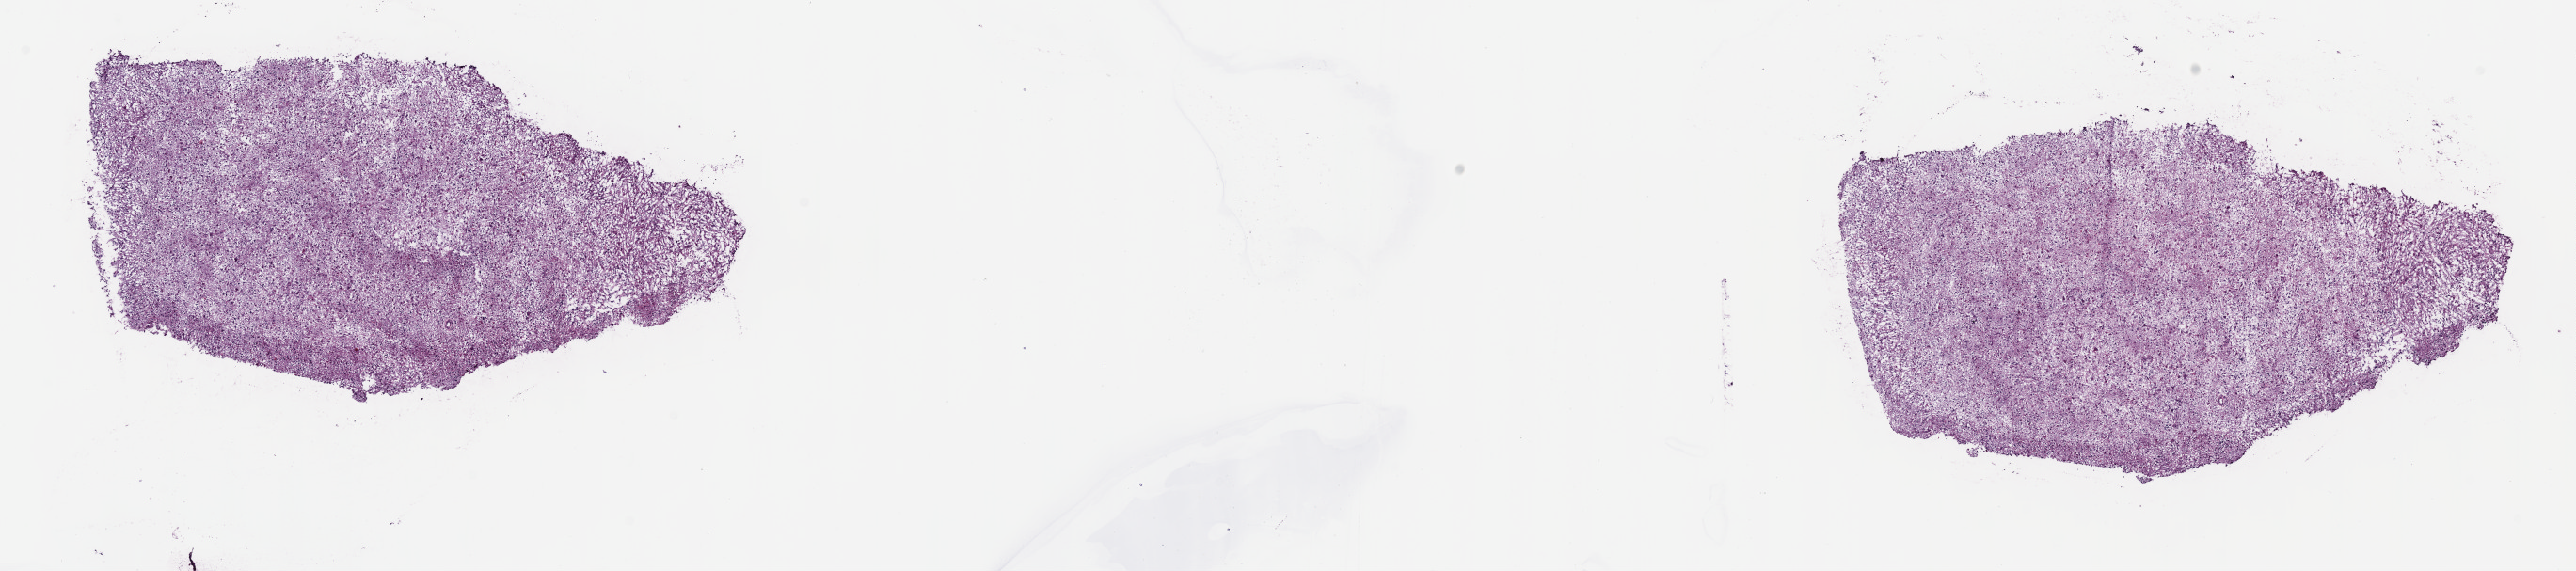
Digitized H&E-stained tissue section (whole slide) — shown as a low-resolution overview of the whole scanned area (about 22.1 x 4.9 mm, acquisition: 40x scan), frozen section from the top of the tissue portion, sample: primary tumour, brain. Patient: female, age at initial diagnosis 32 years. Histologic grade: G3 (poorly differentiated). Slide review estimates, as recorded: tumour cells 40%, tumour nuclei 85%, normal cells 5%, stromal cells 55%, necrosis 0%. Infiltration values recorded for this section: lymphocyte infiltration 0%, monocyte infiltration 0%, neutrophil infiltration 0%.
Diagnosis: Astrocytoma, anaplastic (cerebrum).